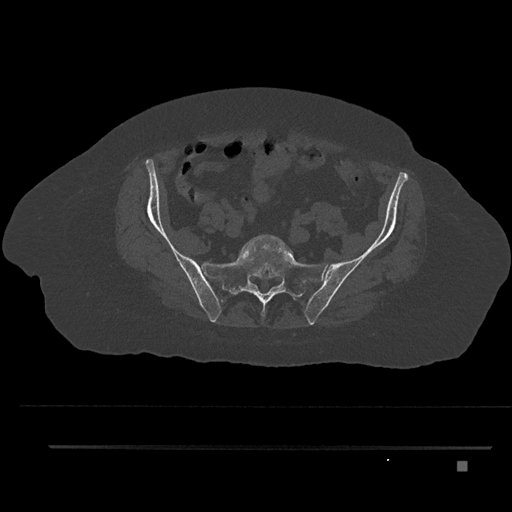
CT including the spine, one axial slice; position 3 of 797 along the scan axis; bone window (W 1800 / L 400 HU); 512 × 512 image matrix, field of view 437 × 437 mm. Female patient, age 76 years. From the clinical record (not read from this slice): primary cancer: lung; vertebrae with lytic lesions (as recorded): T11, L3.
Outlined on this slice (semi-automatic segmentation, software-assisted and operator-edited):
- L5 vertebra: box from (x=242, y=235) to (x=293, y=259) px